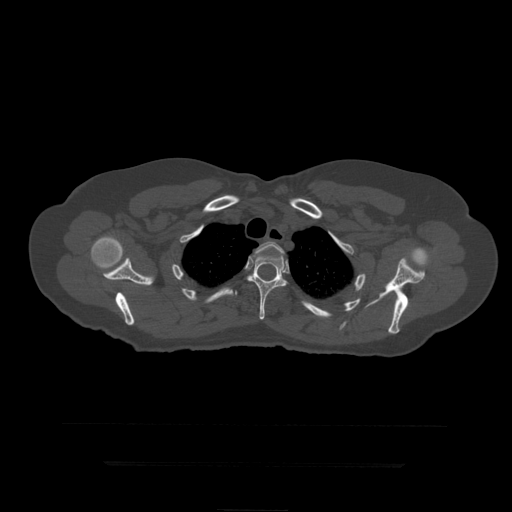
CT including the spine, one axial slice; slice 351 of 399 in the series (ordered by position); reconstruction kernel STANDARD; 120 kVp; bone window (W 1800 / L 400 HU); 1.25 mm slice thickness; 512 × 512 image matrix, field of view 450 × 450 mm. Patient age 41 years. Case-level facts recorded for this patient, not image findings: primary cancer: breast.
Outlined on this slice (semi-automatically segmented with operator editing):
- T3 vertebra: bounding box (x1, y1, x2, y2) in pixels: (252, 242, 285, 258)
- T4 vertebra: (247, 254, 289, 320)
- T5 vertebra: (235, 291, 238, 296)